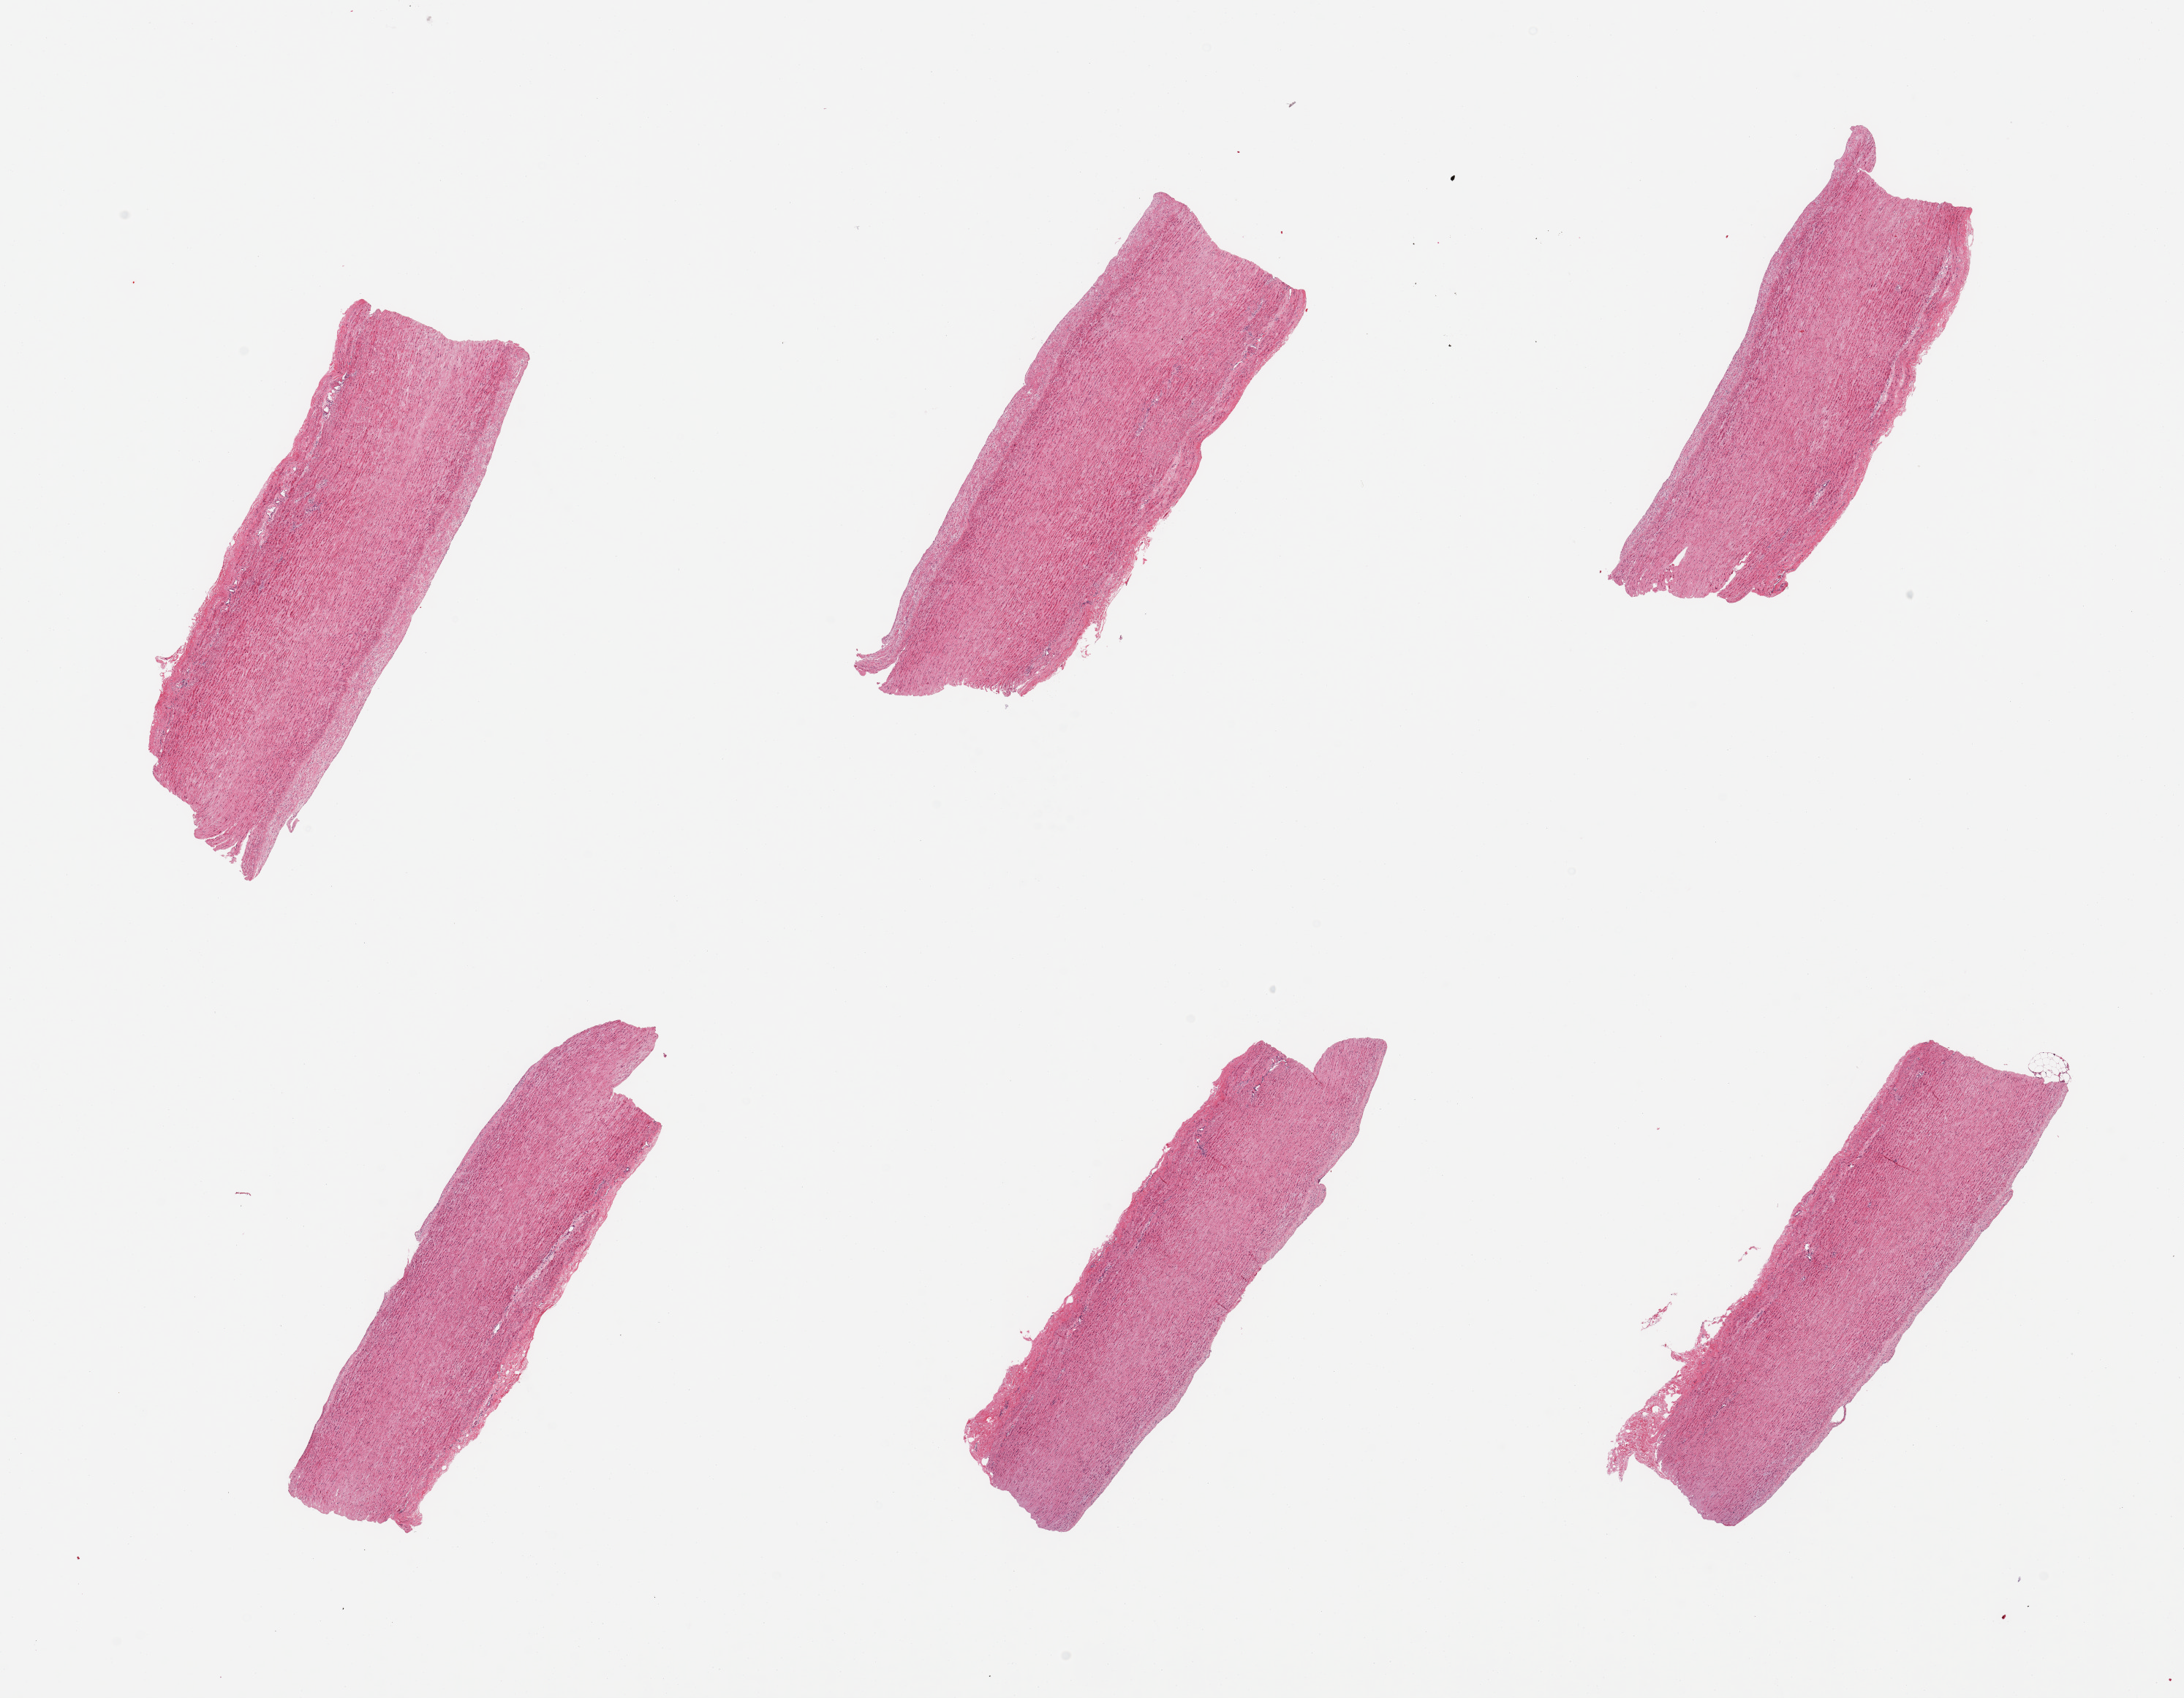
Digitized H&E-stained section, shown as a low-resolution overview of the whole scanned area (about 23.6 x 18.4 mm, from a 20x scan), PAXgene-fixed paraffin-embedded (PFPE) section, target tissue: aorta, tissue donor sample.
Review note (as recorded): 6 pieces; mild atherosclerosis.